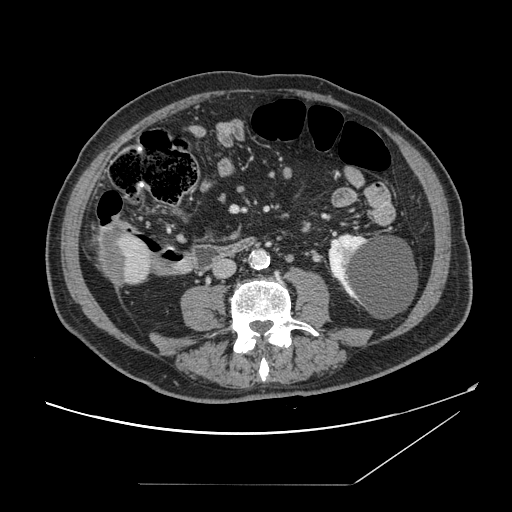
Contrast-enhanced abdominal CT, one axial slice. Slice 27 of 166 in the series (ordered by position). 120 kVp. Intravenous contrast given. Soft-tissue window (W 400 / L 40 HU). 2.5 mm slice thickness. 512 × 512 image matrix, field of view 416 × 416 mm. Male patient, age 80 years. Case-level facts recorded for this patient, not image findings: diagnosis: colorectal cancer liver metastases, imaged before liver resection; multiple liver metastases: no; largest metastasis: 2.2 cm; chemotherapy before resection: no.
Annotated regions visible in this slice (outlined manually by an expert reader):
- liver: bounding box <98,227,153,287> (left, top, right, bottom; pixels)
- liver metastasis: <100,232,130,284>